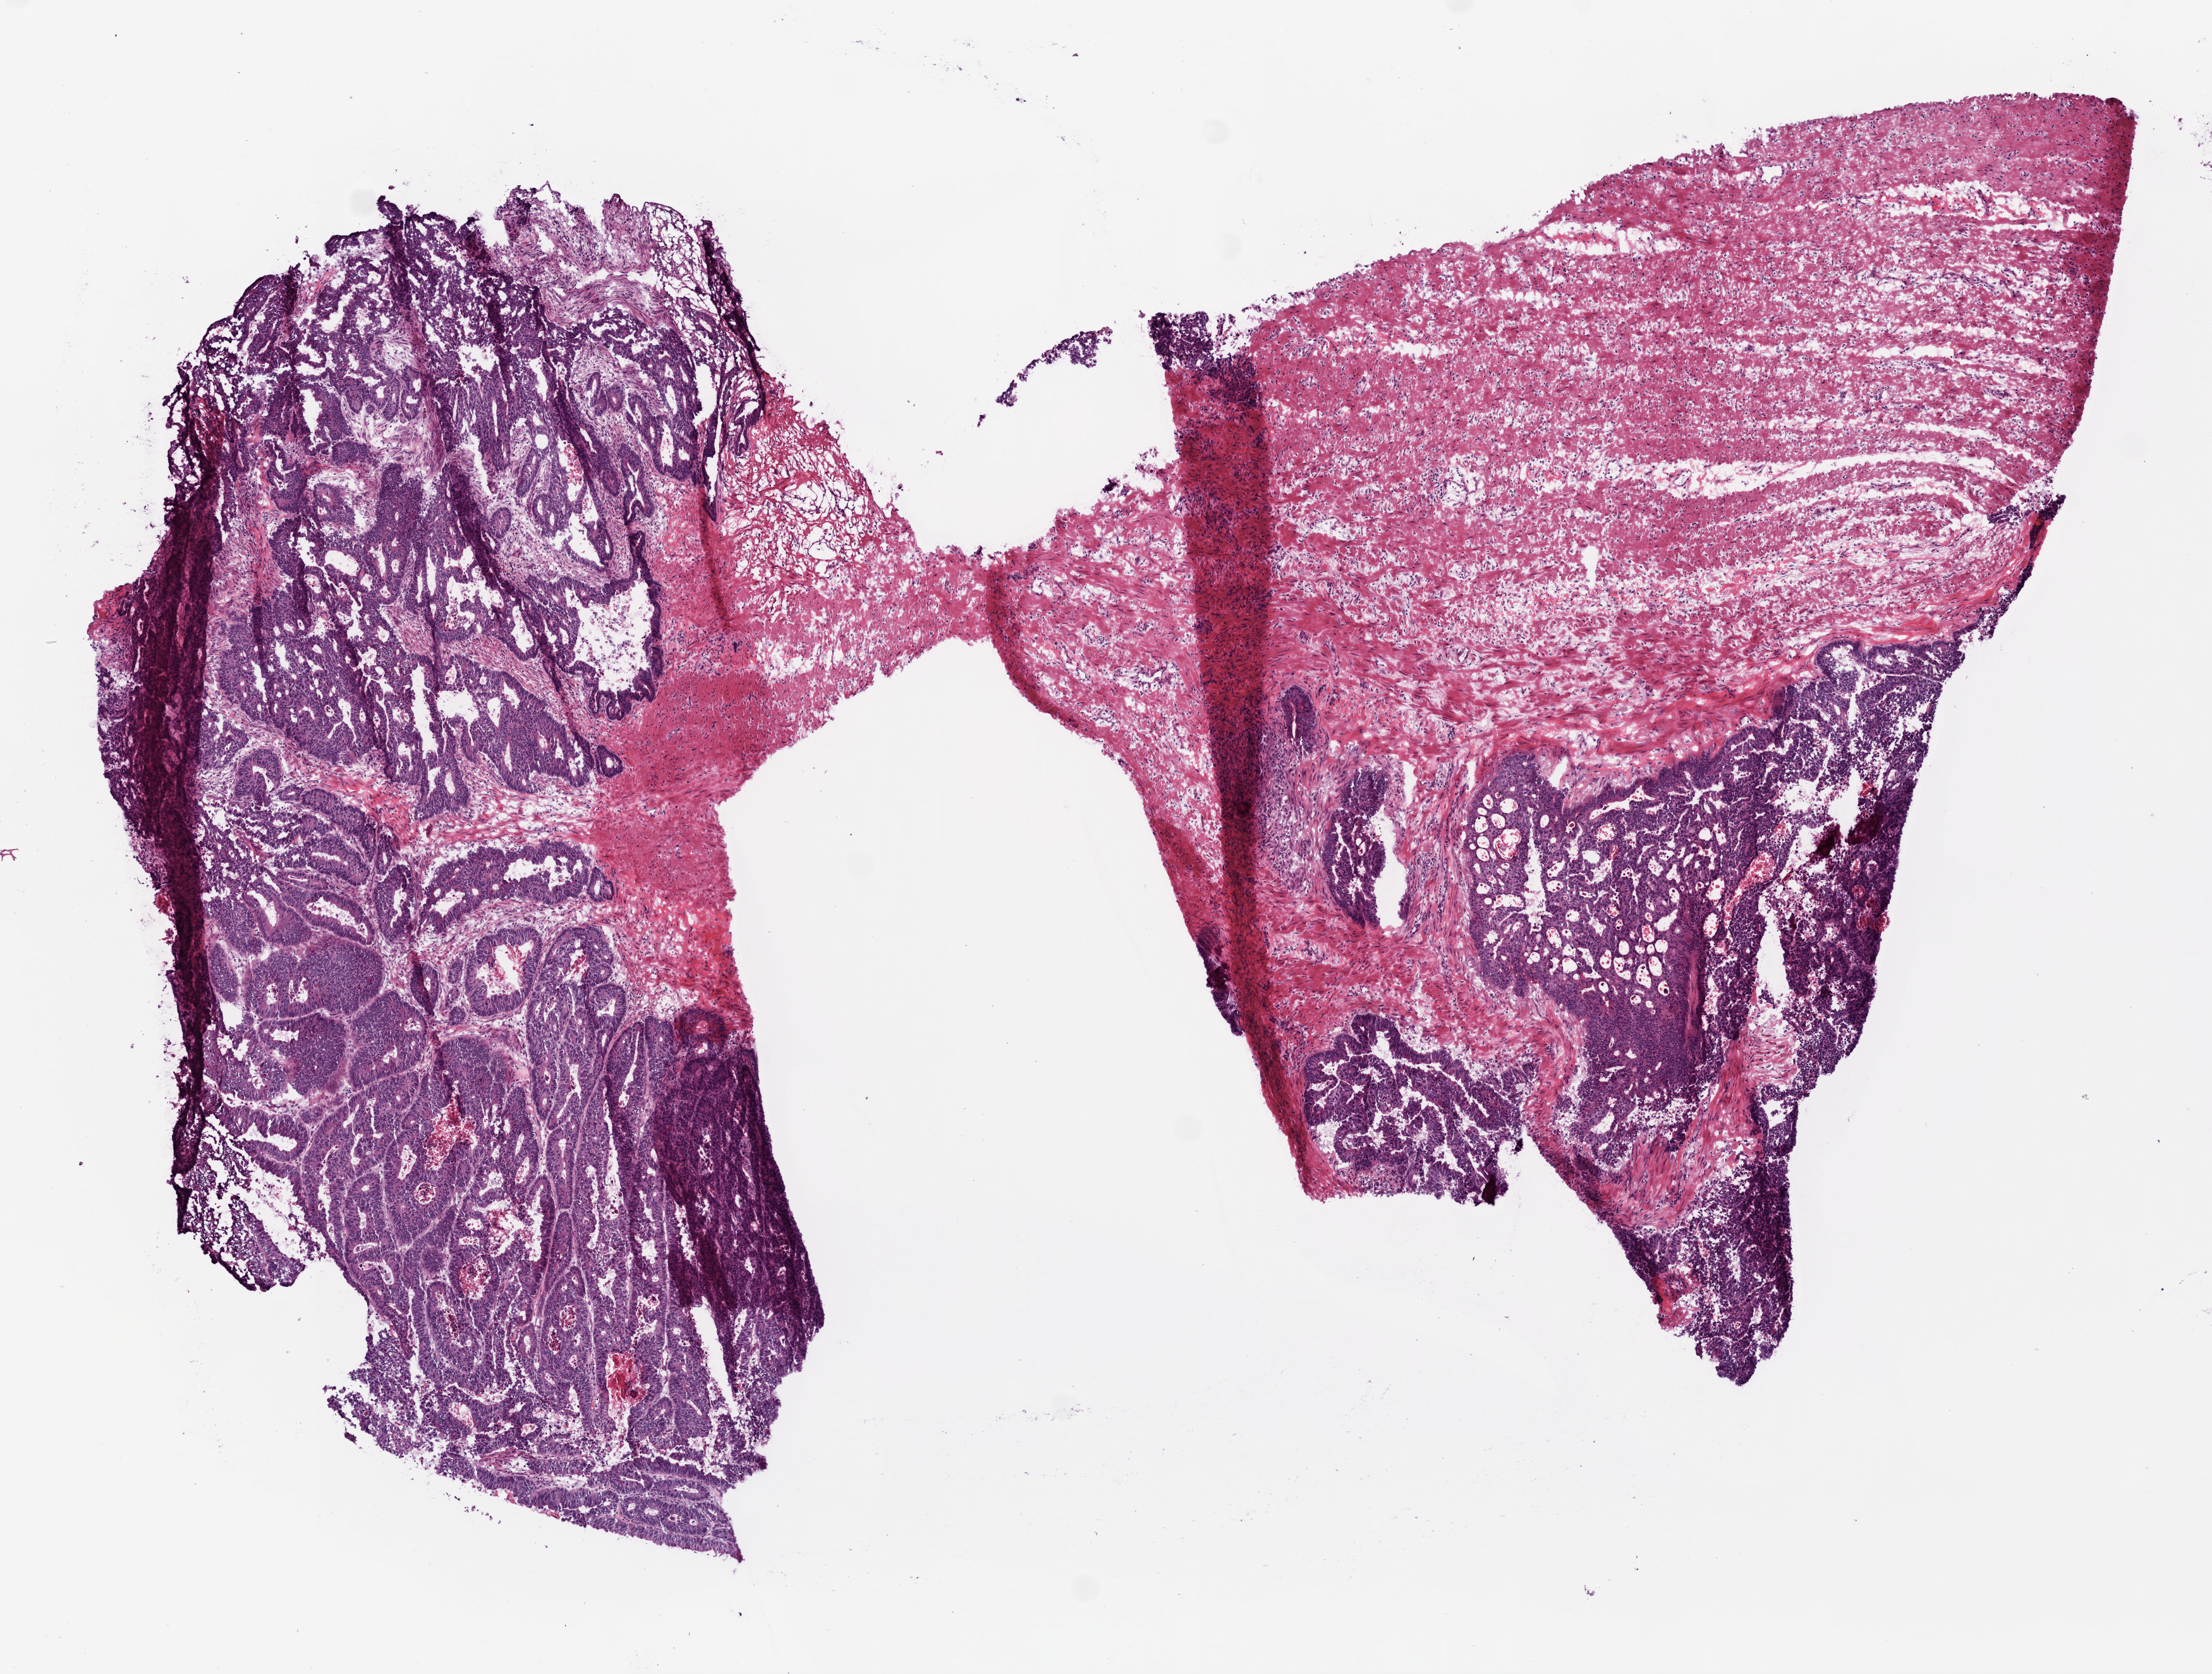
Digitized H&E tissue section (whole slide) — a low-resolution overview of the entire scanned area, about 7.0 x 5.3 mm, frozen section from the bottom of the tissue portion, colon, primary tumour sample. Patient: female, age at initial diagnosis 77 years. Slide review estimates, as recorded: tumour cells 42%, tumour nuclei 75%, normal cells 0%, stromal cells 50%, necrosis 8%.
• diagnosis: Adenocarcinoma, NOS (sigmoid colon)
• AJCC pathologic stage: IV (6th edition)